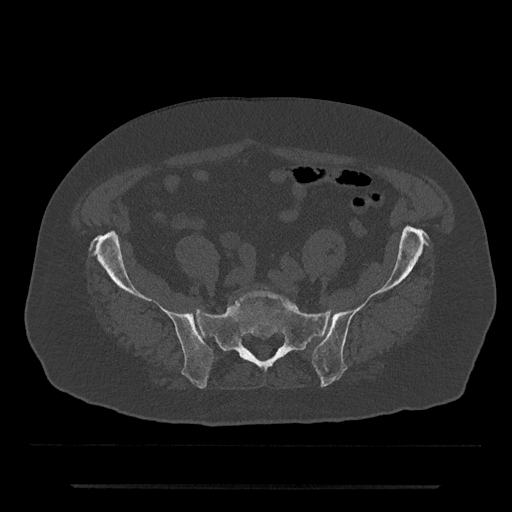
CT including the spine, one axial slice. Position 236 of 797 along the scan axis. Reconstruction kernel Br40s/3. 120 kVp. Bone window (W 1800 / L 400 HU). 0.5 mm slice thickness. 512 × 512 image matrix, field of view 434 × 434 mm. Patient: male, 80 years. From the clinical record (not read from this slice): primary cancer: prostate; vertebrae with lytic lesions (as recorded): L1, T11.
Structures marked on this image (semi-automatically segmented with operator editing):
- L5 vertebra: bounding box (x1, y1, x2, y2) in pixels: (235, 290, 299, 311)